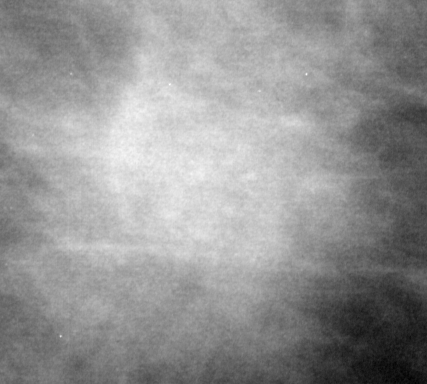
Crop from a digitized film mammogram around one marked abnormality; right breast; MLO view; BI-RADS breast density category 2 (scale 1–4).
Finding: mass, shape irregular, margins spiculated; BI-RADS assessment category 5; pathology result (as recorded, not read from the image): malignant.